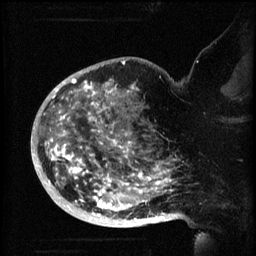
Breast MRI (dynamic contrast-enhanced), one sagittal slice. Position 43 of 60 along the scan axis. 3 images stored at this slice position (order not interpretable as contrast timing). 1.5 T. TE 4.2 ms, TR 8.2 ms. 2 mm slice thickness. 256 × 256 image matrix, field of view 200 × 200 mm. Female patient, age 50 years.
Annotated regions visible in this slice (semi-automatic segmentation, software-assisted and operator-edited):
- analysis volume of interest (the breast-tissue region the enhancement analysis was run in; not a lesion): bounding box <44,72,173,219> (left, top, right, bottom; pixels)
- tumour enhancement mask (voxels above the 70 % enhancement threshold inside the analysis volume of interest): <45,72,173,219>